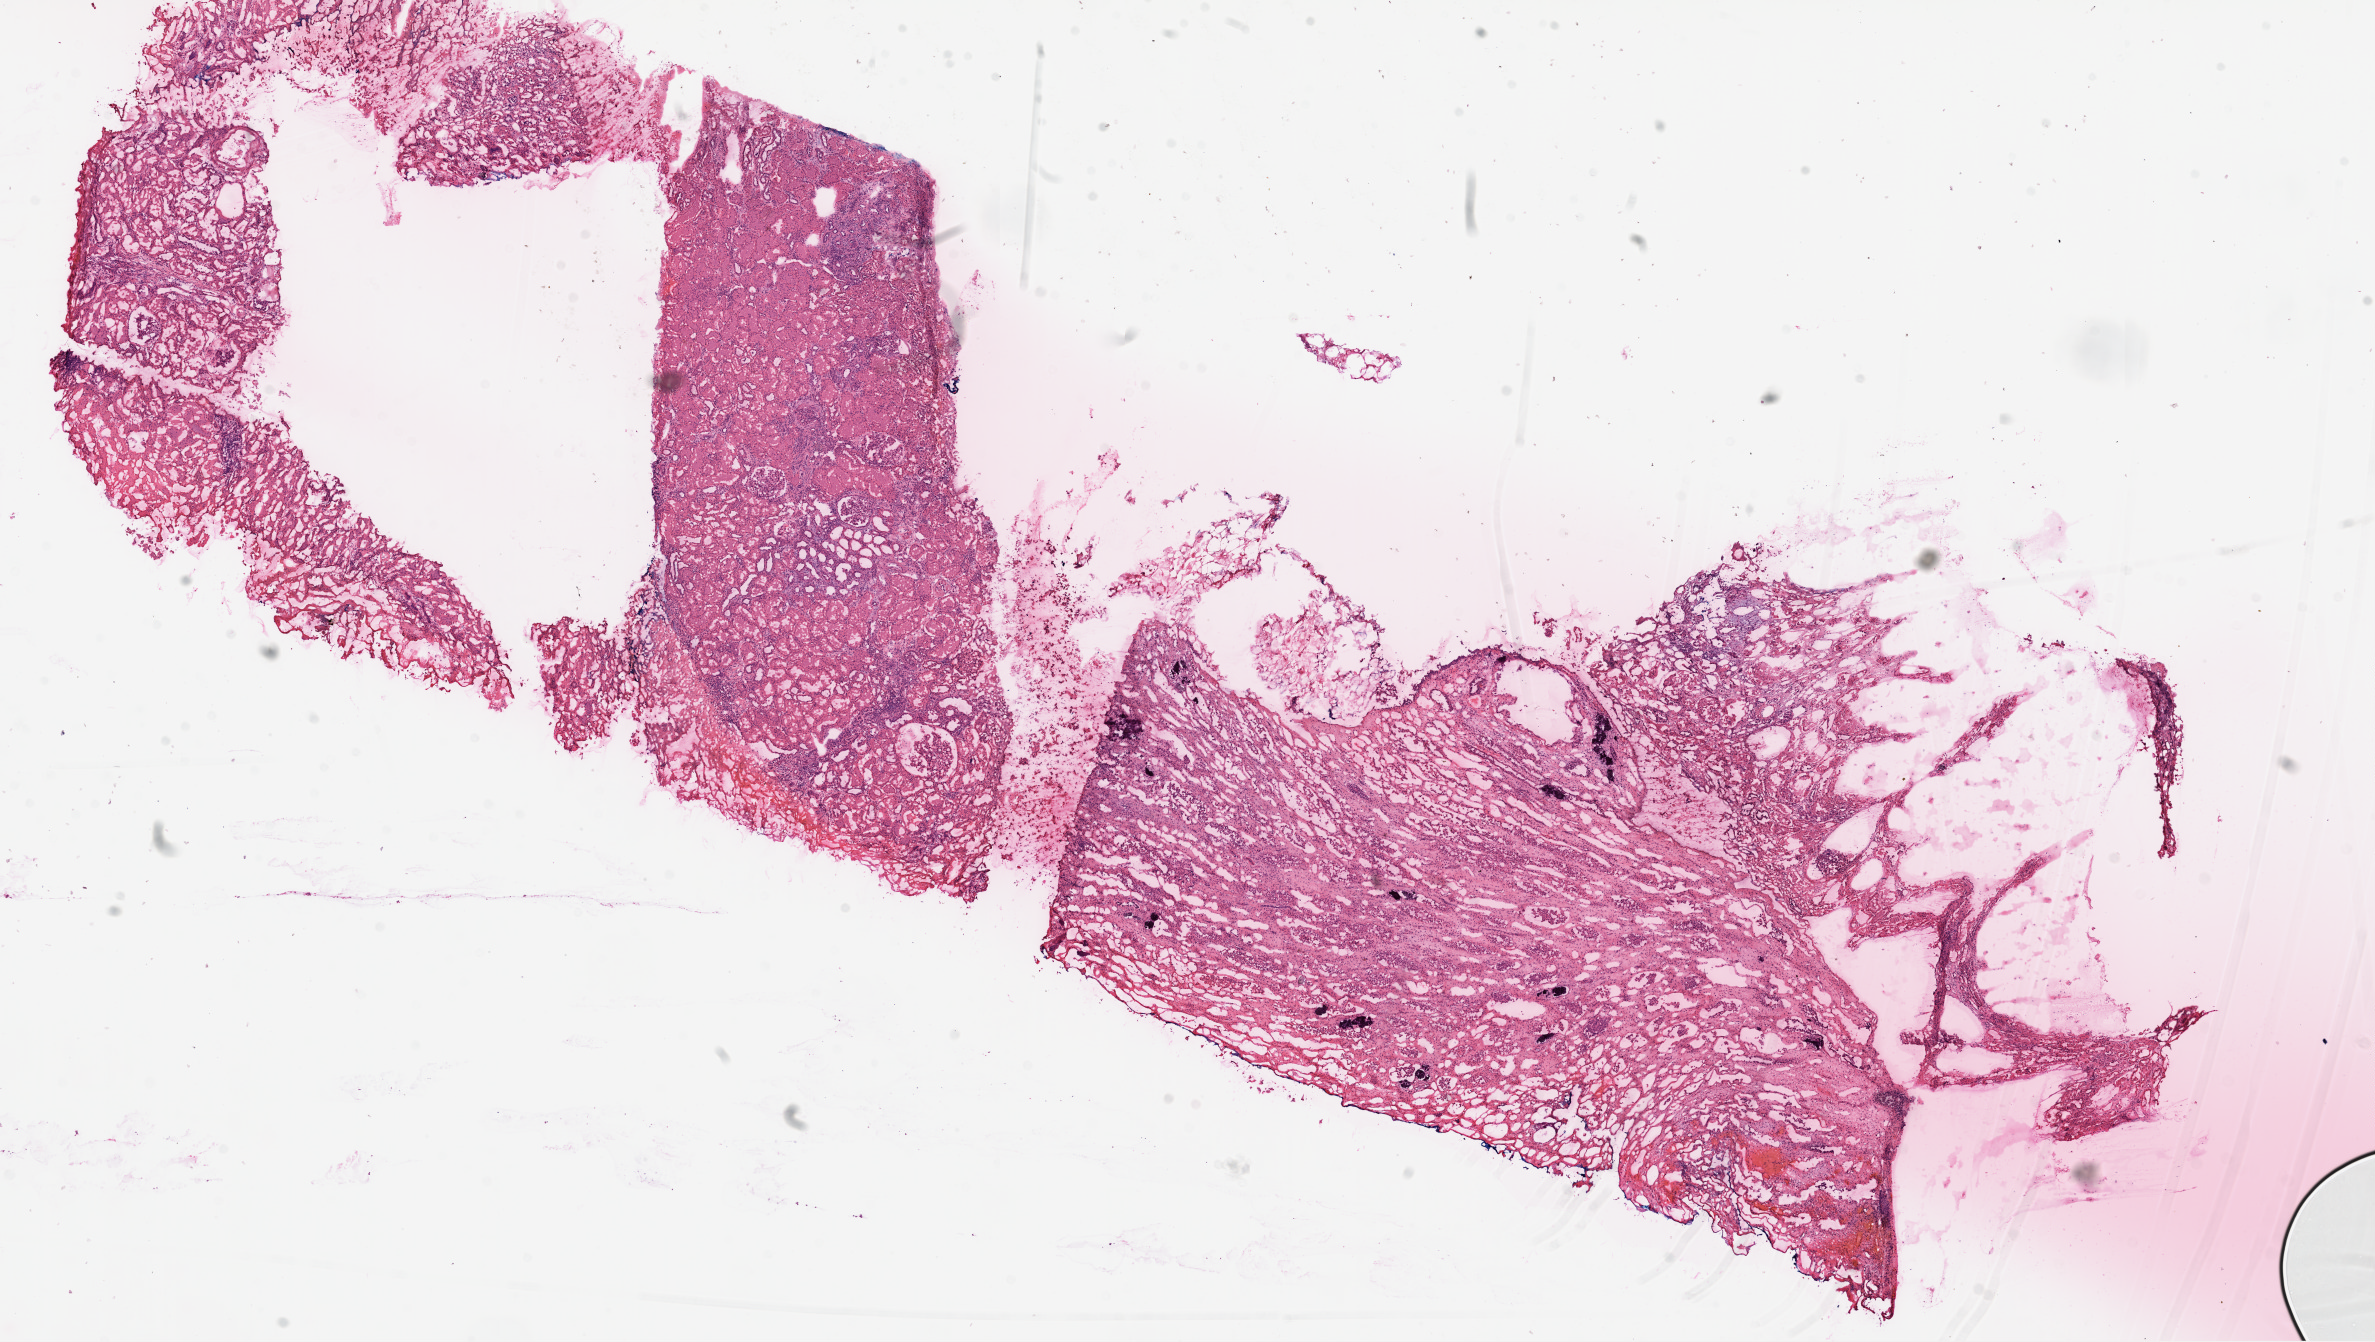
Whole-slide histology image, H&E-stained — whole scanned area (about 19.1 x 10.8 mm) shown as a low-resolution overview; frozen section from the top of the tissue portion; solid tissue normal (non-tumour tissue) sample from the kidney. Patient: male, age at initial diagnosis 58 years.
This section: solid tissue normal sample (biorepository sample class). Patient diagnosis: Clear cell adenocarcinoma, NOS.